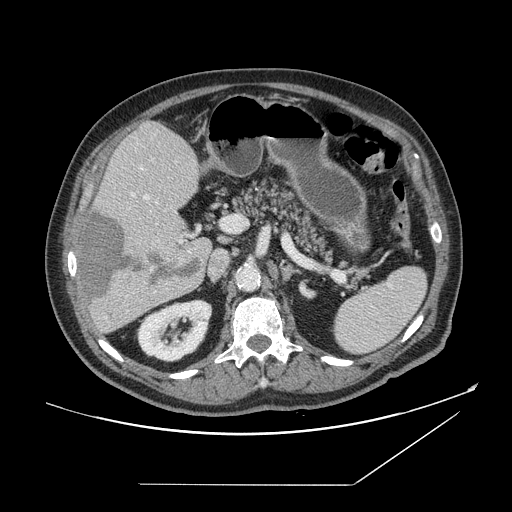
Contrast-enhanced abdominal CT, one axial slice. 120 kVp. Intravenous contrast given. Soft-tissue window (W 400 / L 40 HU). 2.5 mm slice thickness. 512 × 512 image matrix. Male patient, age 80 years. From the clinical record (not read from this slice): diagnosis: colorectal cancer liver metastases, imaged before liver resection; multiple liver metastases: no; largest metastasis: 2.2 cm; disease in both lobes: no.
Annotated regions visible in this slice (manually delineated by an expert):
- hepatic veins: bounding box (x1, y1, x2, y2) in pixels: (140, 167, 152, 270)
- liver: (79, 122, 212, 334)
- planned liver remnant (the part of the liver to remain after resection): (99, 122, 210, 247)
- portal vein (with intrahepatic branches): (132, 193, 231, 243)
- liver metastasis: (83, 211, 204, 302)